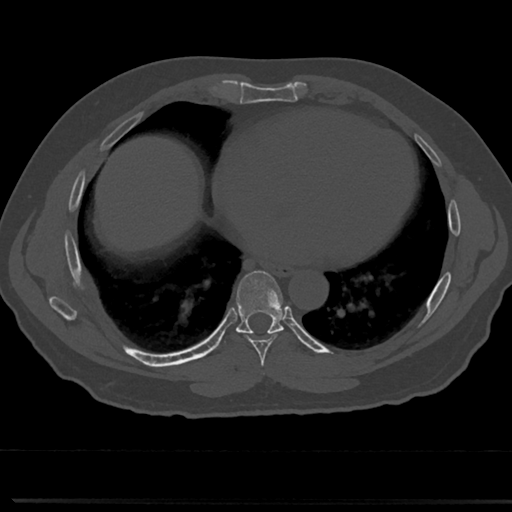
CT including the spine, one axial slice. Position 377 of 817 along the scan axis. 120 kVp. Bone window (W 1800 / L 400 HU). 0.5 mm slice thickness. 512 × 512 image matrix, field of view 355 × 355 mm. Patient: male, 61 years. Case-level facts recorded for this patient, not image findings: primary cancer: prostate.
Structures marked on this image (semi-automatically segmented with operator editing):
- T6 vertebra: bounding box <261,370,265,374> (left, top, right, bottom; pixels)
- T7 vertebra: <233,272,290,355>
- T8 vertebra: <239,326,280,332>